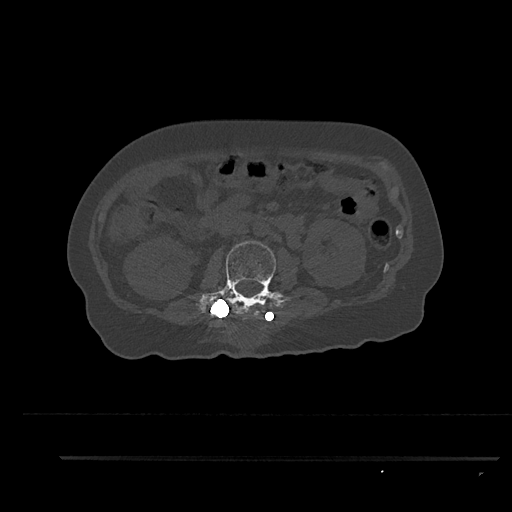
CT including the spine, one axial slice. Position 153 of 797 along the scan axis. Reconstruction kernel Br40s/3. 120 kVp. Bone window (W 1800 / L 400 HU). 512 × 512 image matrix, field of view 408 × 408 mm. Female patient, age 44 years. Case-level facts recorded for this patient, not image findings: primary cancer: renal; vertebrae with lytic lesions (as recorded): L1.
Outlined on this slice (semi-automatic segmentation, software-assisted and operator-edited):
- L2 vertebra: bounding box (x1, y1, x2, y2) in pixels: (196, 240, 282, 319)